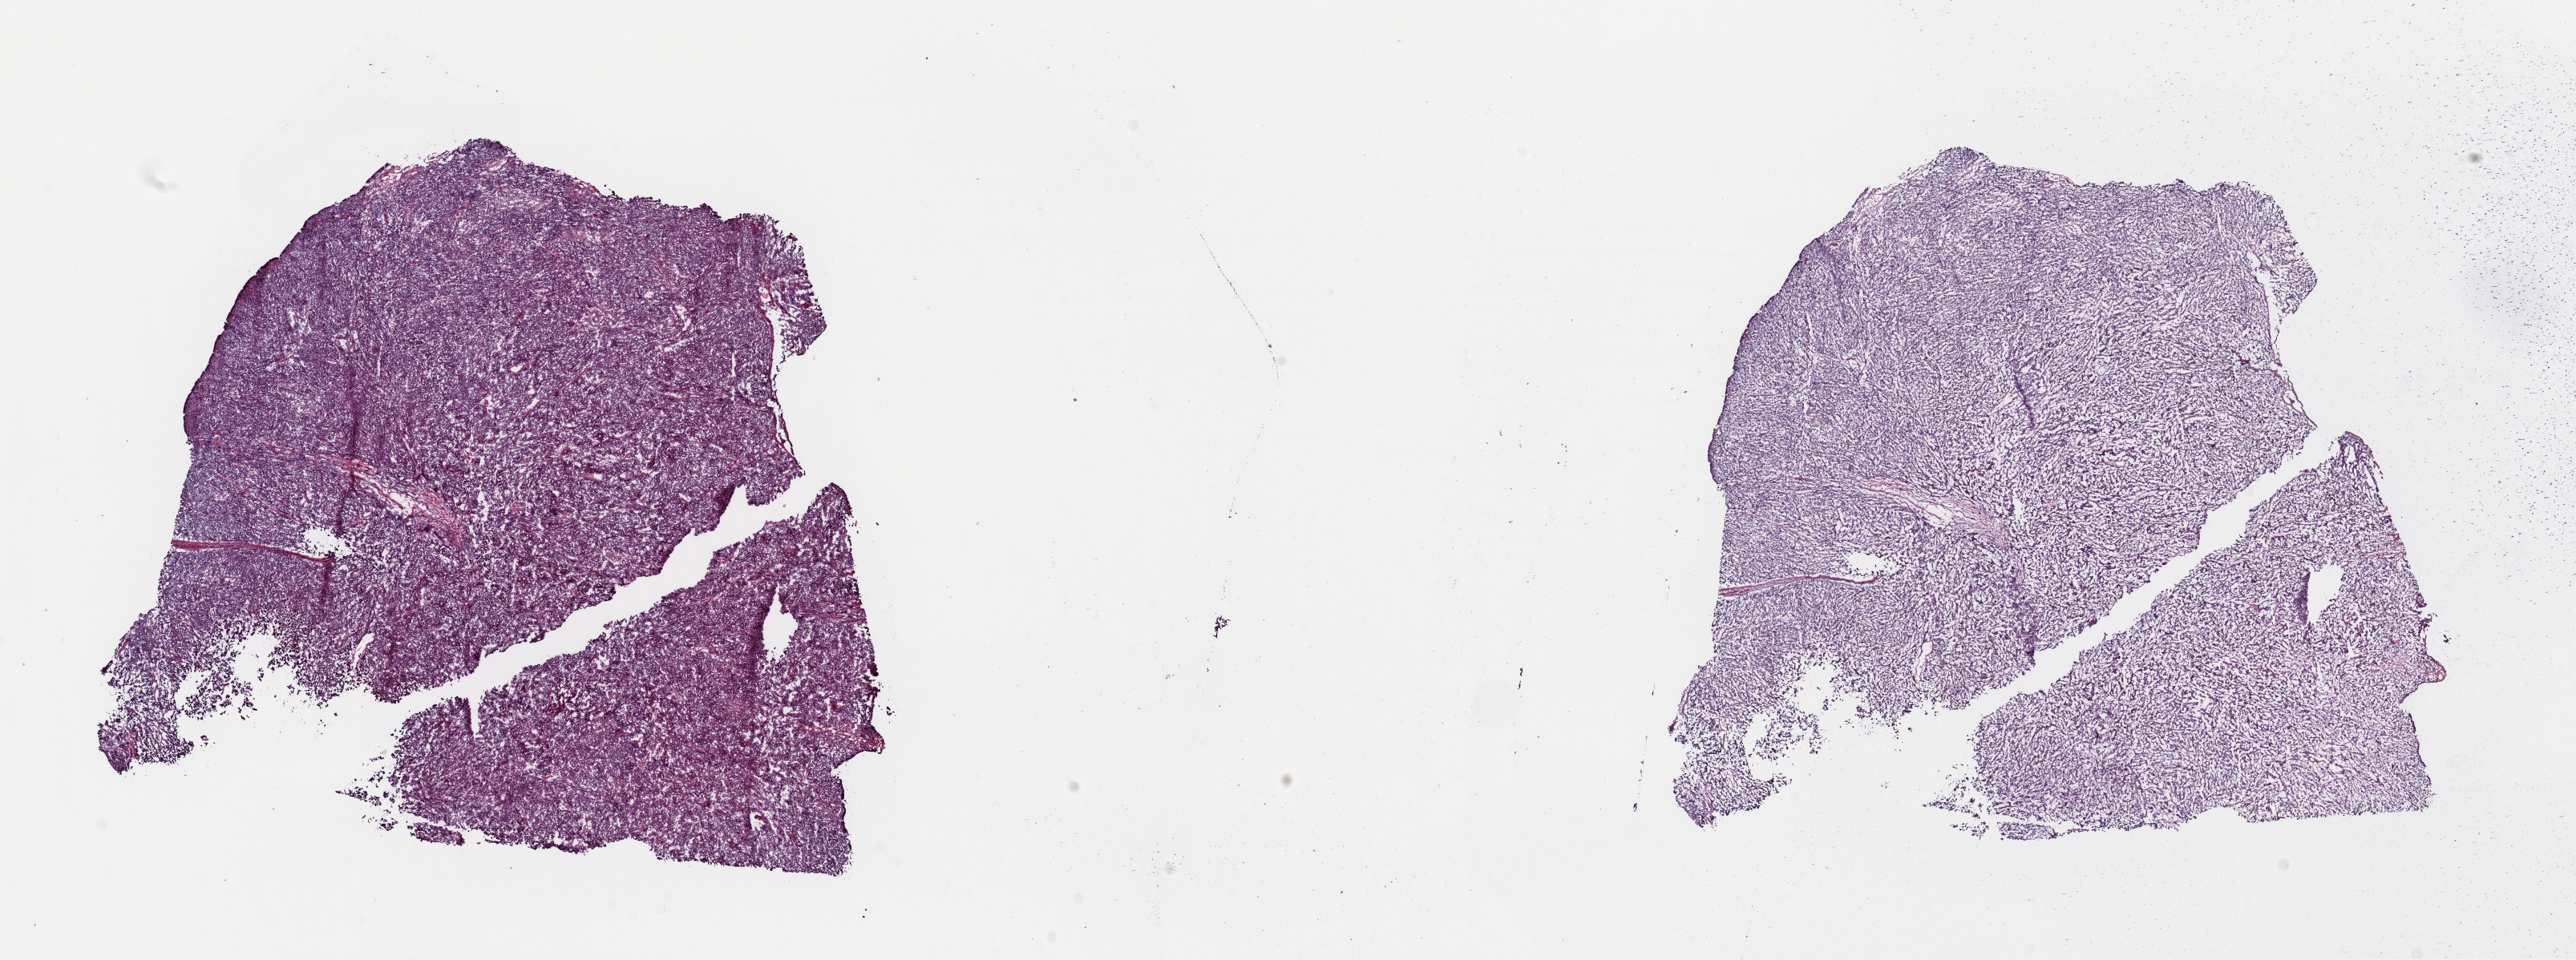
Whole-slide histology image, Hematoxylin and eosin (H&E) stained, shown as a low-resolution overview of the whole scanned area (about 25.4 x 9.5 mm, from a 40x scan), frozen section from the top of the tissue portion, metastatic tumour sample, sampled site: connective, subcutaneous and other soft tissues of lower limb and hip. Female patient; age at initial diagnosis 39 years. Slide review estimates, as recorded: tumour cells 100%, tumour nuclei 85%, normal cells 0%, stromal cells 0%, necrosis 0%. Inflammatory infiltration, as recorded: lymphocyte infiltration 1%, monocyte infiltration 1%, neutrophil infiltration 0%.
This section: metastatic tumour tissue. Patient diagnosis: Malignant melanoma, NOS.